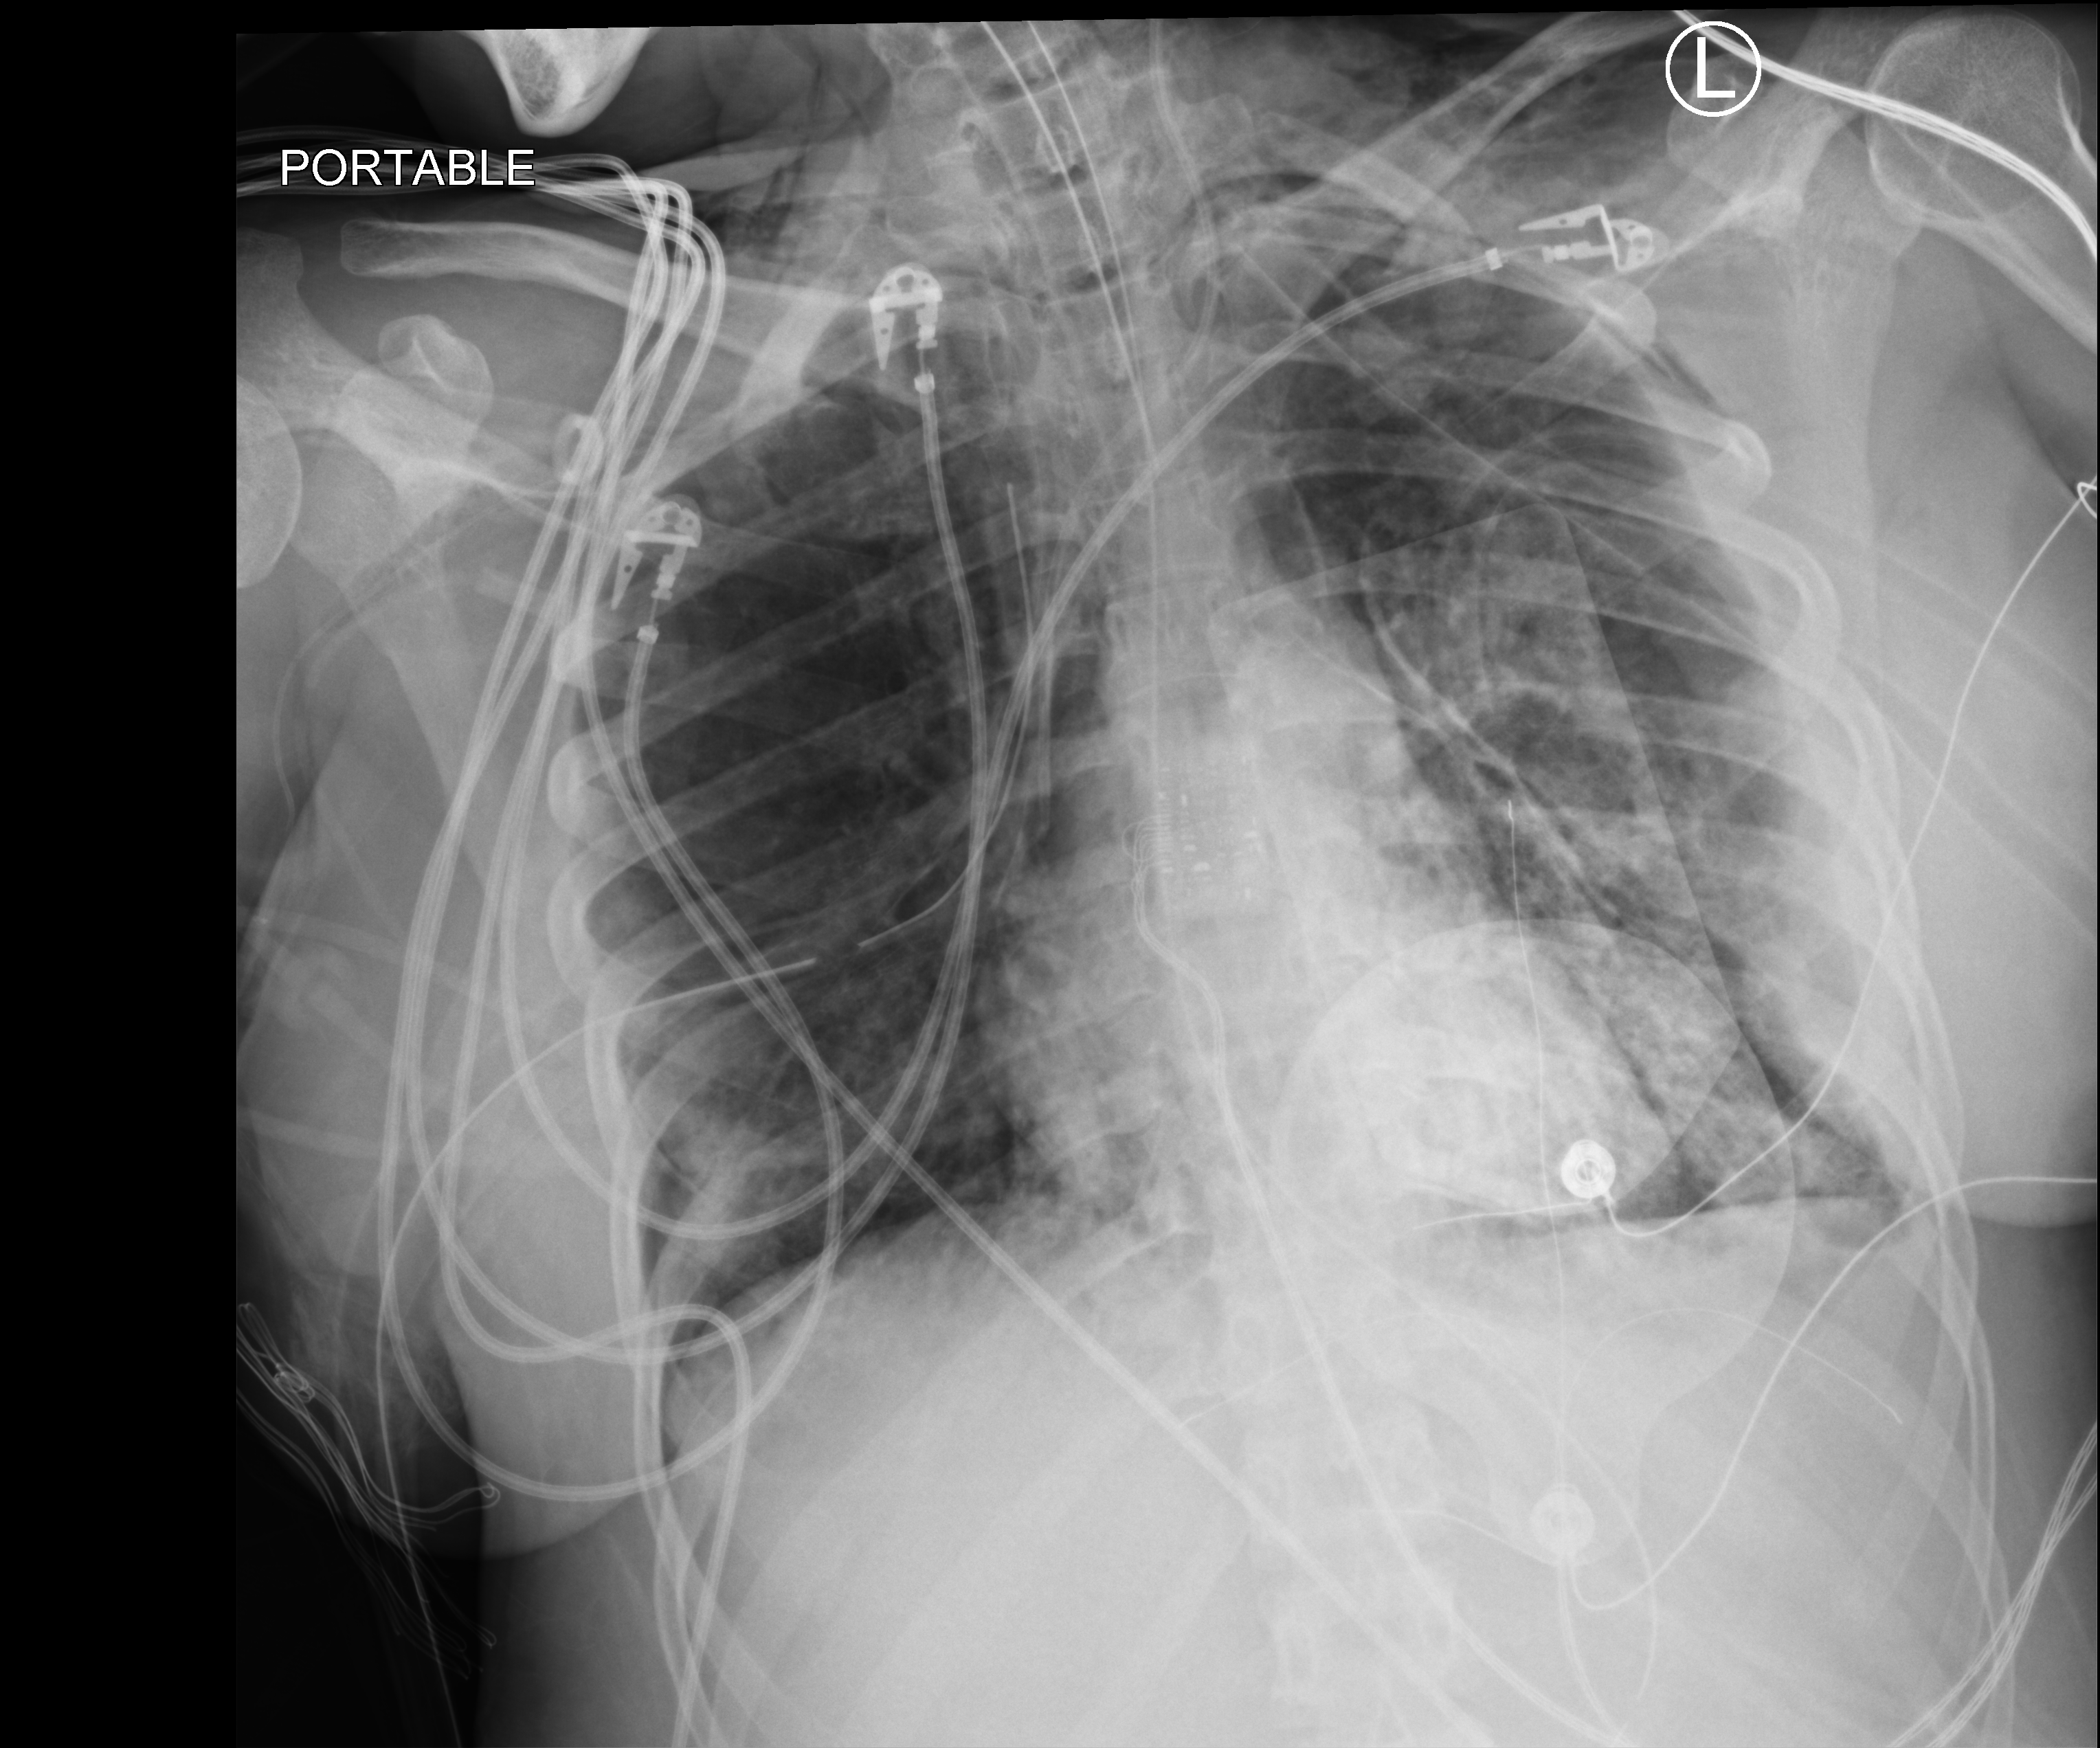
Bedside chest radiograph (computed radiography); anteroposterior (AP) projection. Adult patient hospitalised with COVID-19, age 18–59 years.
Admission-level facts for this patient (not findings on this image; timing relative to this image not recorded):
- admitted to intensive care during this hospital stay: yes
- mechanically ventilated during this hospital stay: yes